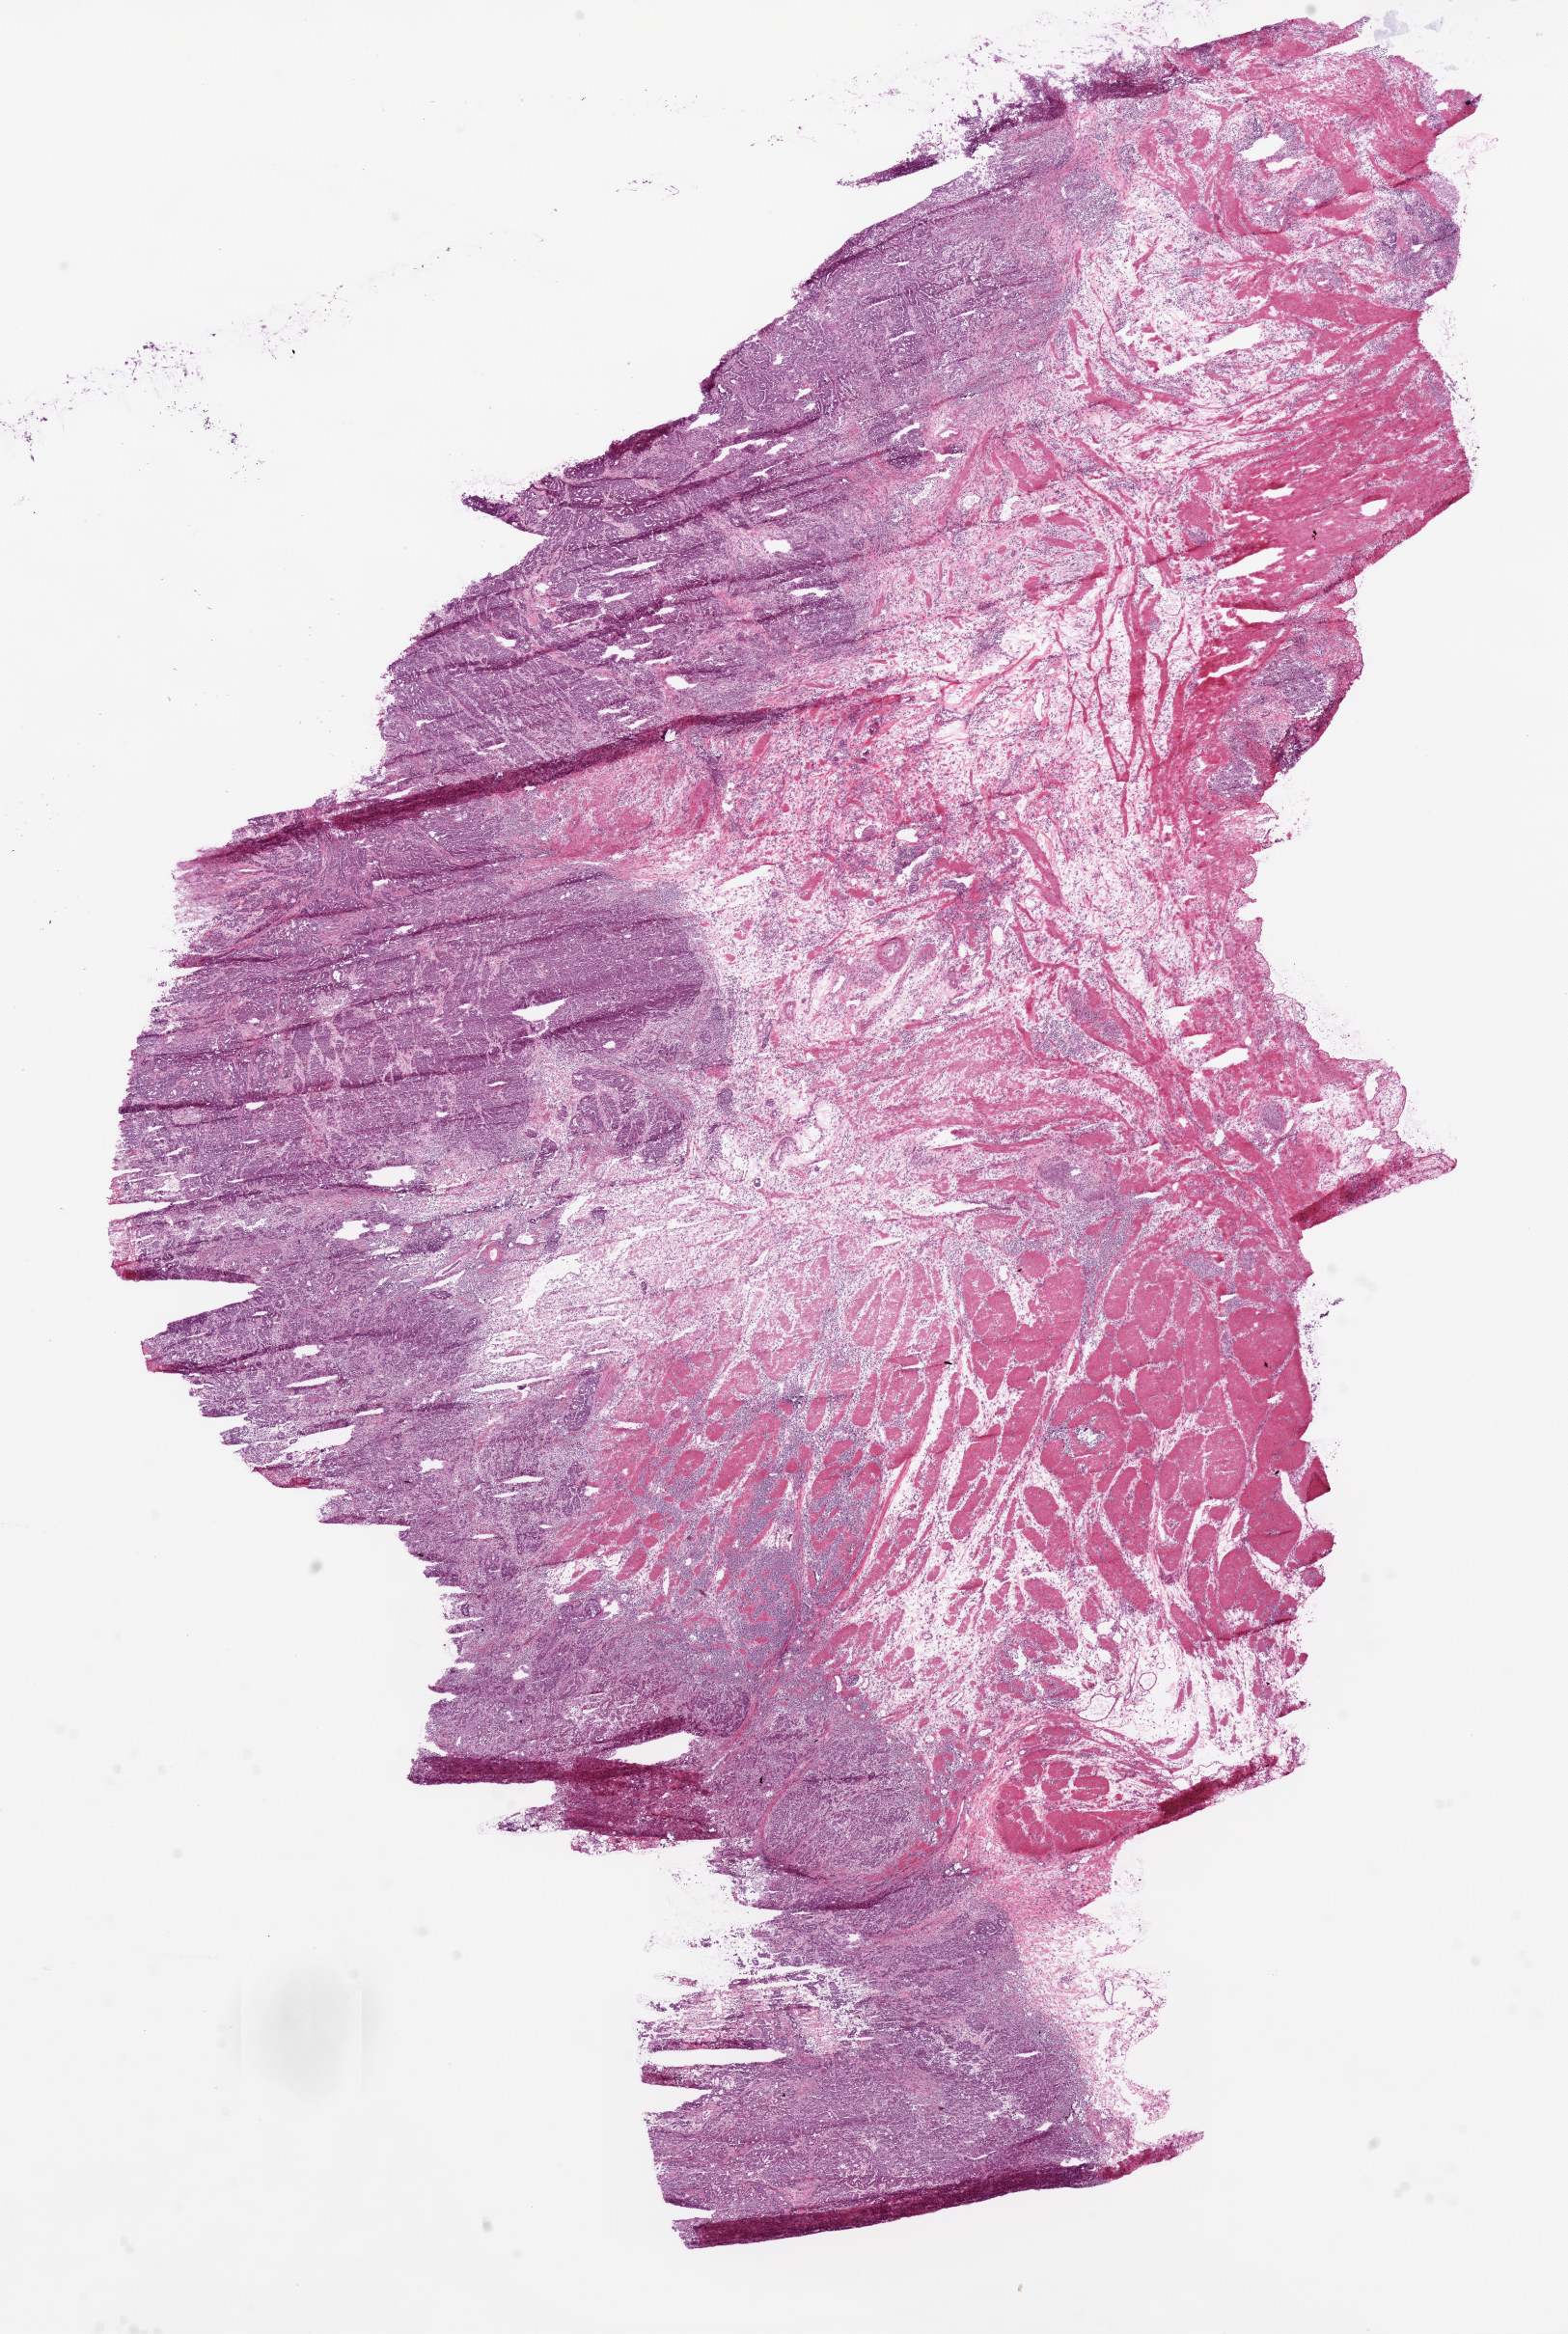
Digitized Hematoxylin and eosin (H&E) stained tissue section (whole slide) — whole scanned area (about 13.0 x 19.4 mm, from a 20x scan) shown as a low-resolution overview, frozen section, stomach, primary tumour sample. Patient: male, age at initial diagnosis 80 years. Histologic grade: G2 (moderately differentiated). Pathologist review of this section (percent, as recorded): tumour cells 67%, tumour nuclei 80%, normal cells 10%, stromal cells 20%, necrosis 3%.
- pathologic diagnosis: Adenocarcinoma, NOS (gastric antrum)